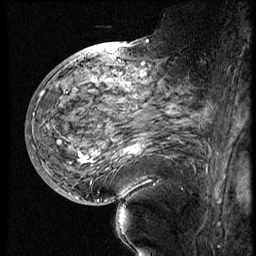
Breast MRI (dynamic contrast-enhanced), one sagittal slice; position 31 of 60 along the scan axis; 4 images stored at this slice position (order not interpretable as contrast timing); 1.5 T; TE 4.2 ms, TR 9 ms; 2.5 mm slice thickness; 256 × 256 image matrix, field of view 180 × 180 mm. Female patient, age 56 years. From the clinical record (not read from this slice): setting: breast cancer imaged before/during neoadjuvant chemotherapy; receptor status: HER2-positive.
Annotated regions visible in this slice (semi-automatically segmented with operator editing):
- analysis volume of interest (the breast-tissue region the enhancement analysis was run in; not a lesion): bounding box <82,83,199,177> (left, top, right, bottom; pixels)
- tumour enhancement mask (voxels above the 140 % enhancement threshold inside the analysis volume of interest): <130,144,145,154>